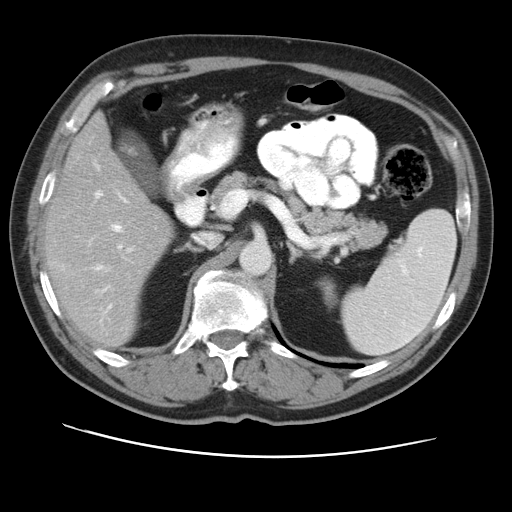
Contrast-enhanced abdominal CT, one axial slice. Slice 26 of 49 in the series (ordered by position). Reconstruction kernel STANDARD. Intravenous contrast given. Soft-tissue window (W 400 / L 40 HU). 5 mm slice thickness. 512 × 512 image matrix. Male patient, age 59 years. Case-level facts recorded for this patient, not image findings: diagnosis: colorectal cancer liver metastases, imaged before liver resection; multiple liver metastases: yes; largest metastasis: 6.3 cm.
Structures marked on this image (expert manual segmentation):
- hepatic veins: bounding box <96,191,217,249> (left, top, right, bottom; pixels)
- liver: <47,118,172,347>
- planned liver remnant (the part of the liver to remain after resection): <48,118,171,347>
- portal vein (with intrahepatic branches): <96,224,132,310>